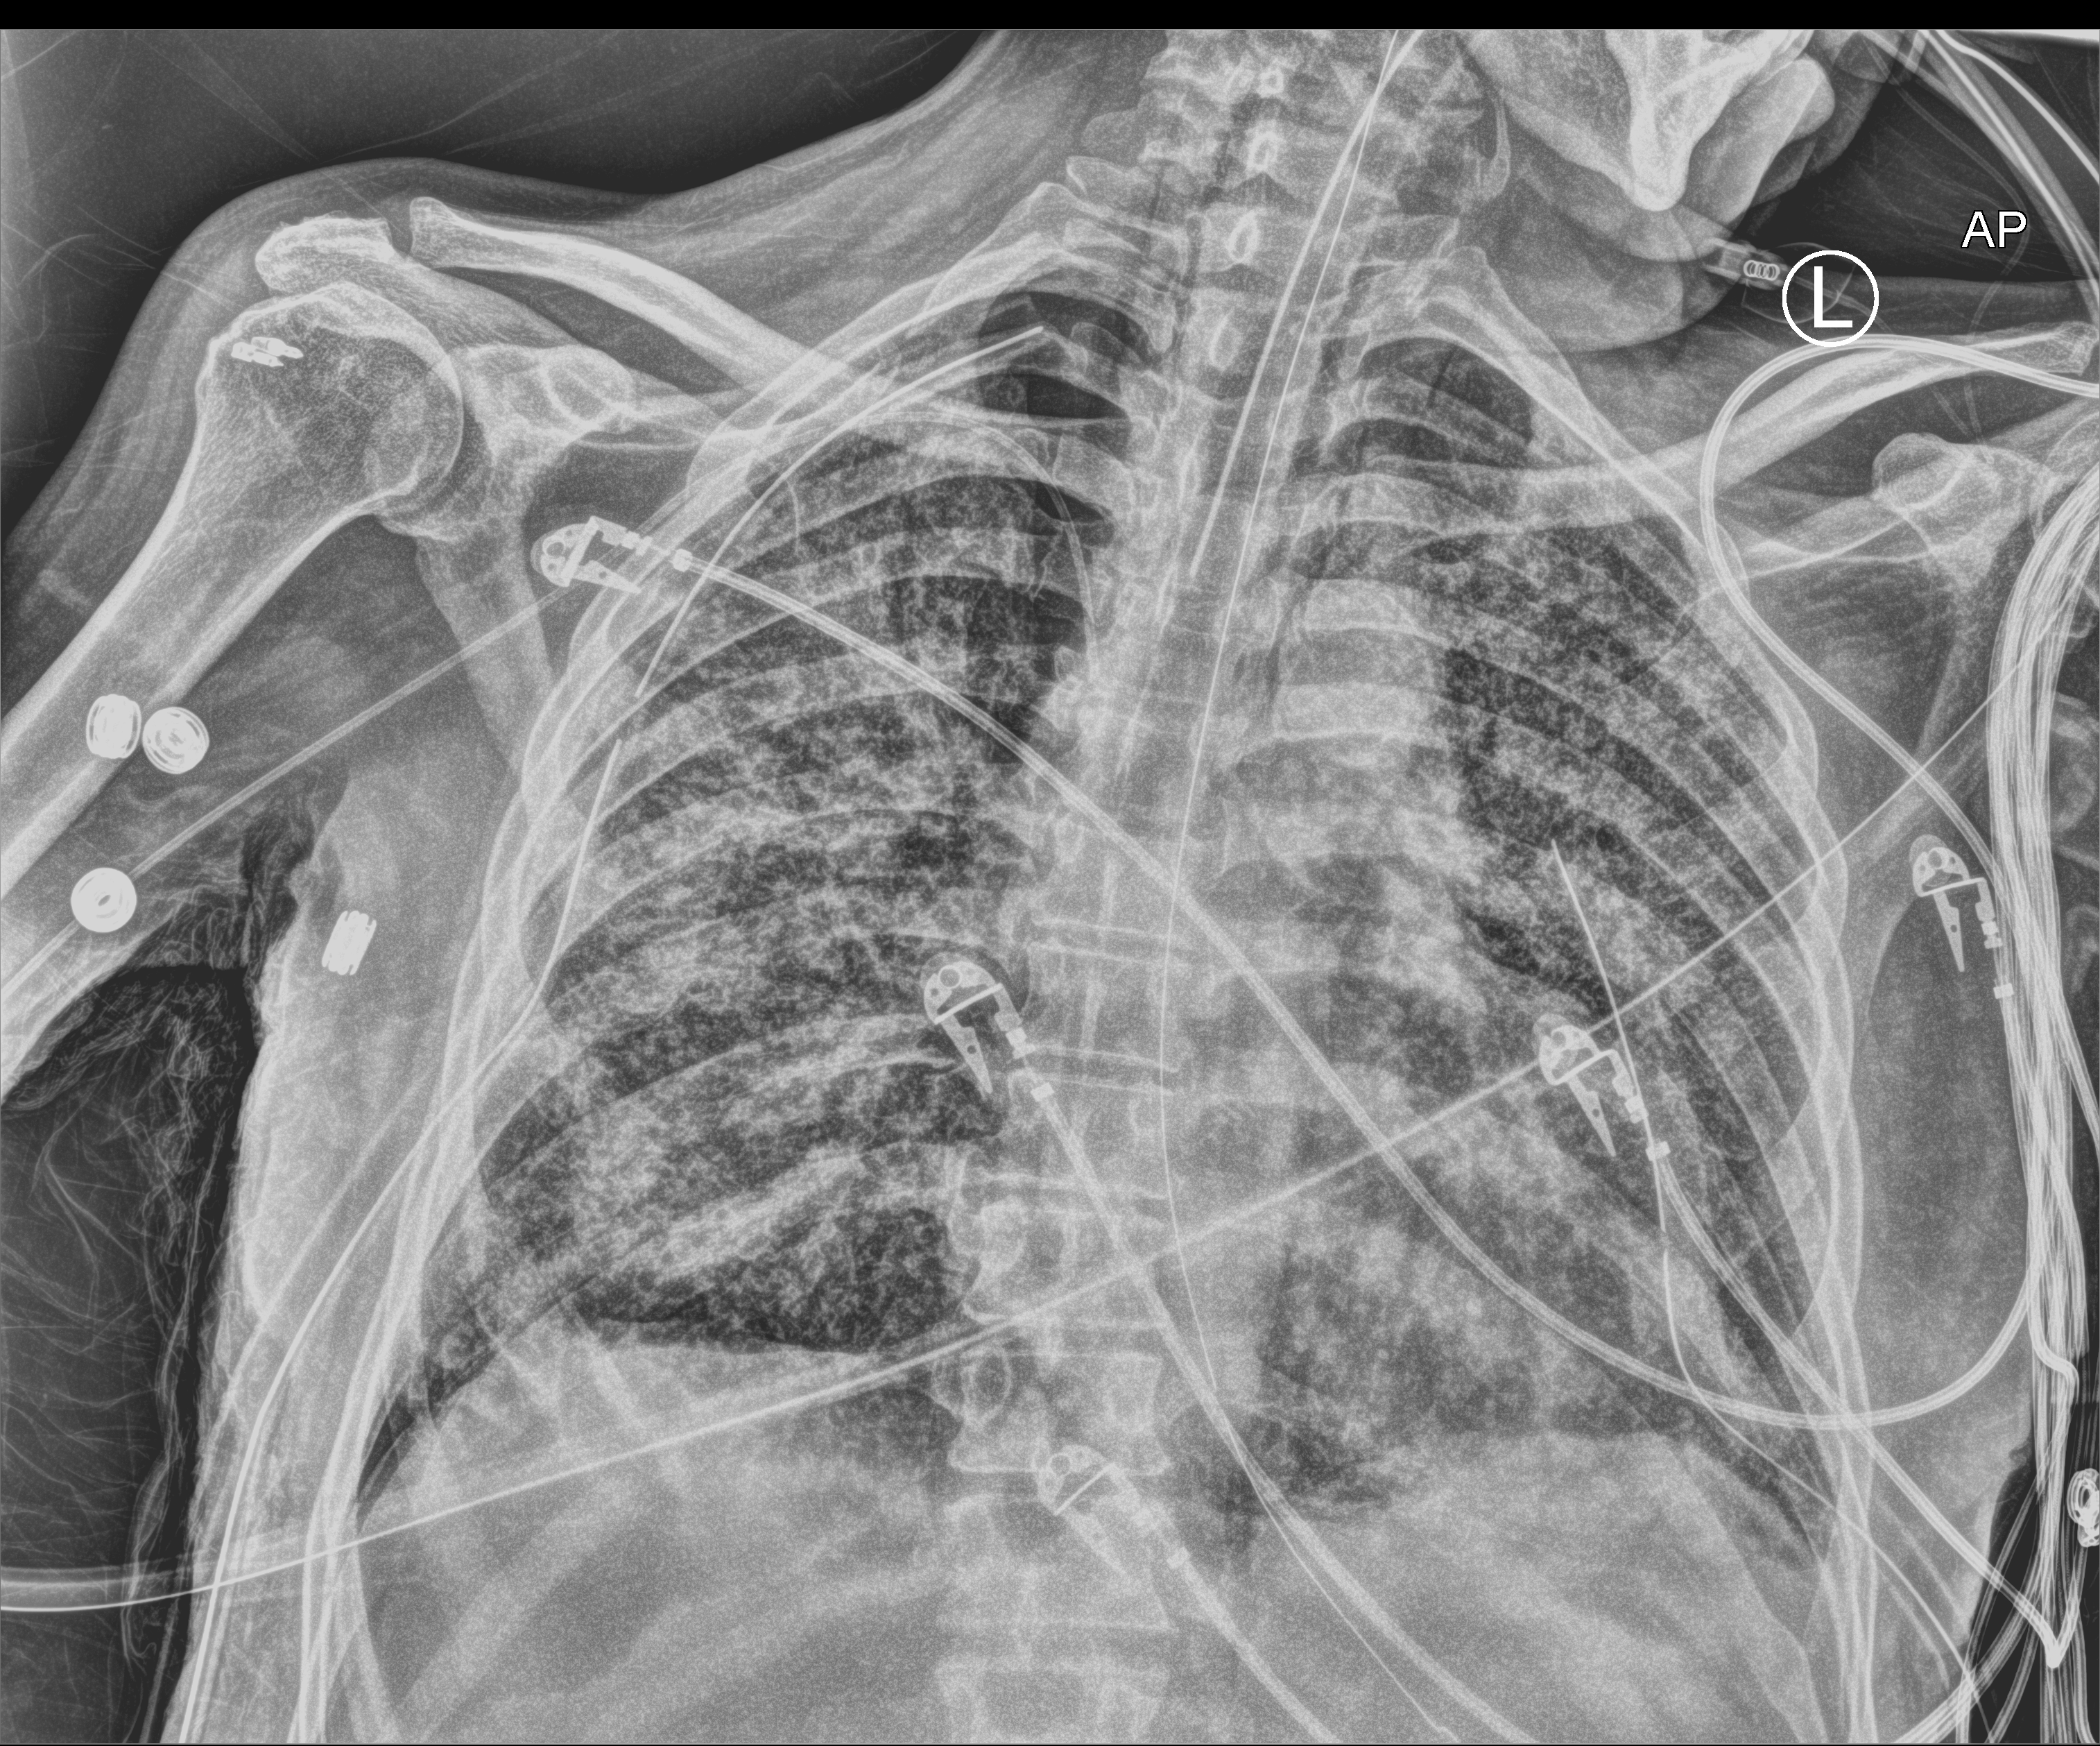
Chest X-ray (portable), anteroposterior (AP) projection. Patient hospitalised with COVID-19; male, aged 60–74 years.
From the hospital-stay record, not from the radiograph (when in the stay this image was taken is not recorded):
- admitted to intensive care during this hospital stay: yes
- mechanically ventilated during this hospital stay: yes